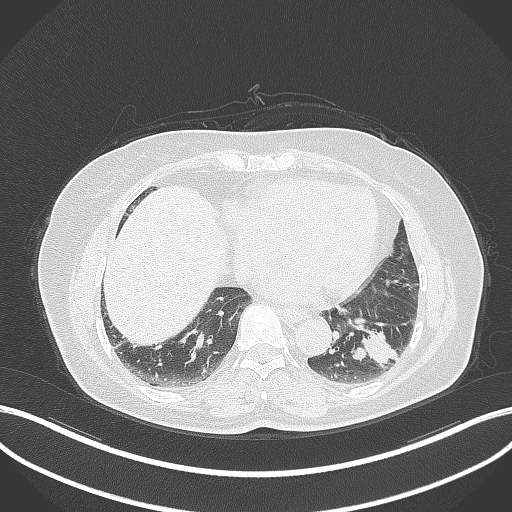
Chest CT, one axial slice. Slice 127 of 311 in the series (ordered by position). Reconstruction kernel B70f. 120 kVp. Lung window (W 1500 / L -600 HU). 1 mm slice thickness. 512 × 512 image matrix, field of view 400 × 400 mm. Female patient, age 59 years. From the clinical record (not read from this slice): clinical TNM (as recorded): T2a N0 M0; histopathological grade: G2-3.
Annotated regions visible in this slice (bounding box drawn by a radiologist):
- lung tumour (recorded histology: adenocarcinoma): bounding box [x1, y1, x2, y2] px = [351, 325, 405, 372]